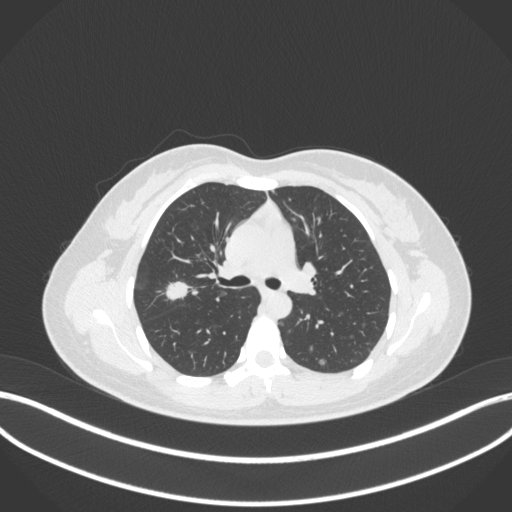
Chest CT, one axial slice; slice 214 of 214 in the series (ordered by position); lung window (W 1500 / L -600 HU); 1 mm slice thickness; 512 × 512 image matrix. Female patient, age 33 years. From the clinical record (not read from this slice): clinical TNM (as recorded): T1c N0 M0; histopathological grade: G2-G3.
Structures marked on this image (bounding box drawn by a radiologist):
- lung tumour (recorded histology: adenocarcinoma): bounding box (x1, y1, x2, y2) in pixels: (160, 274, 194, 307)